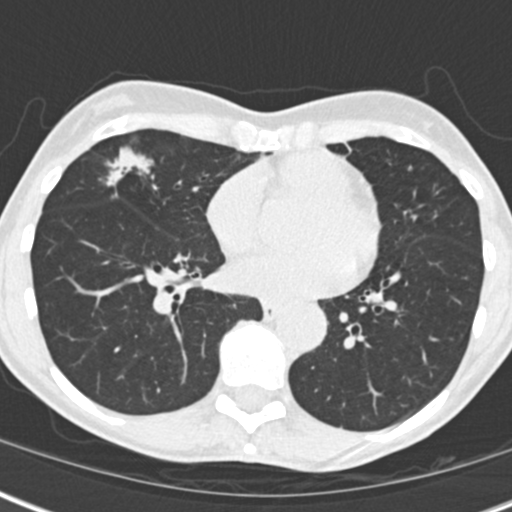
Low-dose screening chest CT, one axial slice; position 71 of 173 along the scan axis; lung window (W 1500 / L -600 HU); 512 × 512 image matrix, field of view 290 × 290 mm.
Annotated regions visible in this slice (outlined manually by an expert reader):
- lesion 1 (tumor, middle lobe of right lung): bounding box [x1, y1, x2, y2] px = [109, 148, 150, 185]